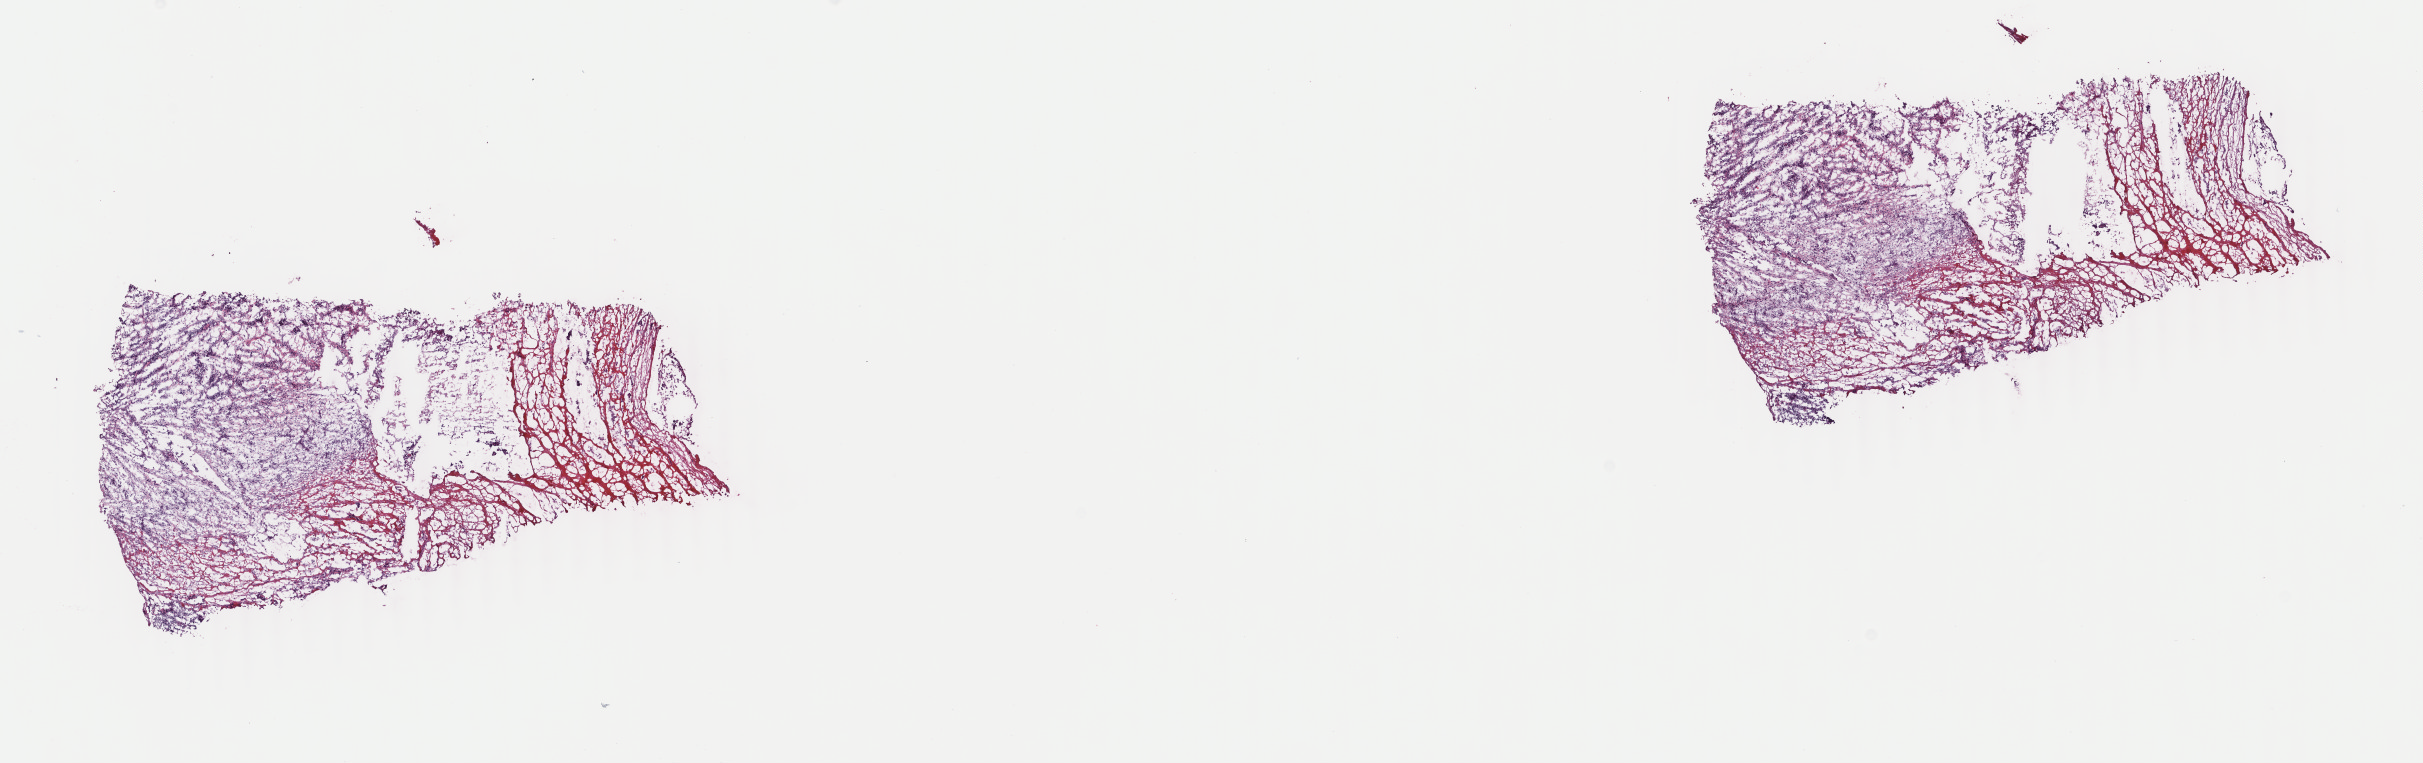
H&E-stained whole-slide image — a low-resolution overview of the entire scanned area, about 19.3 x 6.1 mm (from a 40x scan), frozen section from the top of the tissue portion, mesothelium, primary tumour sample. Patient: male, age at initial diagnosis 57 years. Composition of this section per pathologist review: tumour cells 60%, tumour nuclei 60%, normal cells 0%, stromal cells 20%, necrosis 20%. Infiltration values recorded for this section: lymphocyte infiltration 40%, monocyte infiltration 20%, neutrophil infiltration 20%.
* pathologic diagnosis: Epithelioid mesothelioma, malignant (pleura, NOS)
* AJCC pathologic stage: III (6th edition)